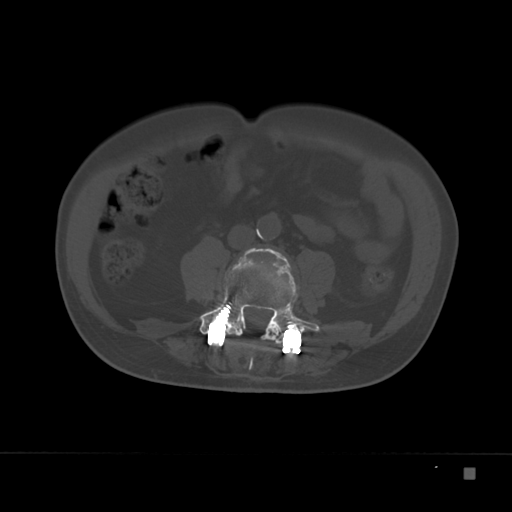
CT including the spine, one axial slice; reconstruction kernel Br40s; 120 kVp; bone window (W 1800 / L 400 HU); 1.5 mm slice thickness; 512 × 512 image matrix, field of view 389 × 389 mm. Patient: male, 72 years. Case-level facts recorded for this patient, not image findings: primary cancer: skeletal.
Annotated regions visible in this slice (semi-automatic segmentation, software-assisted and operator-edited):
- L3 vertebra: box from (x=247, y=248) to (x=292, y=270) px
- L4 vertebra: (x=200, y=248)–(x=322, y=346)